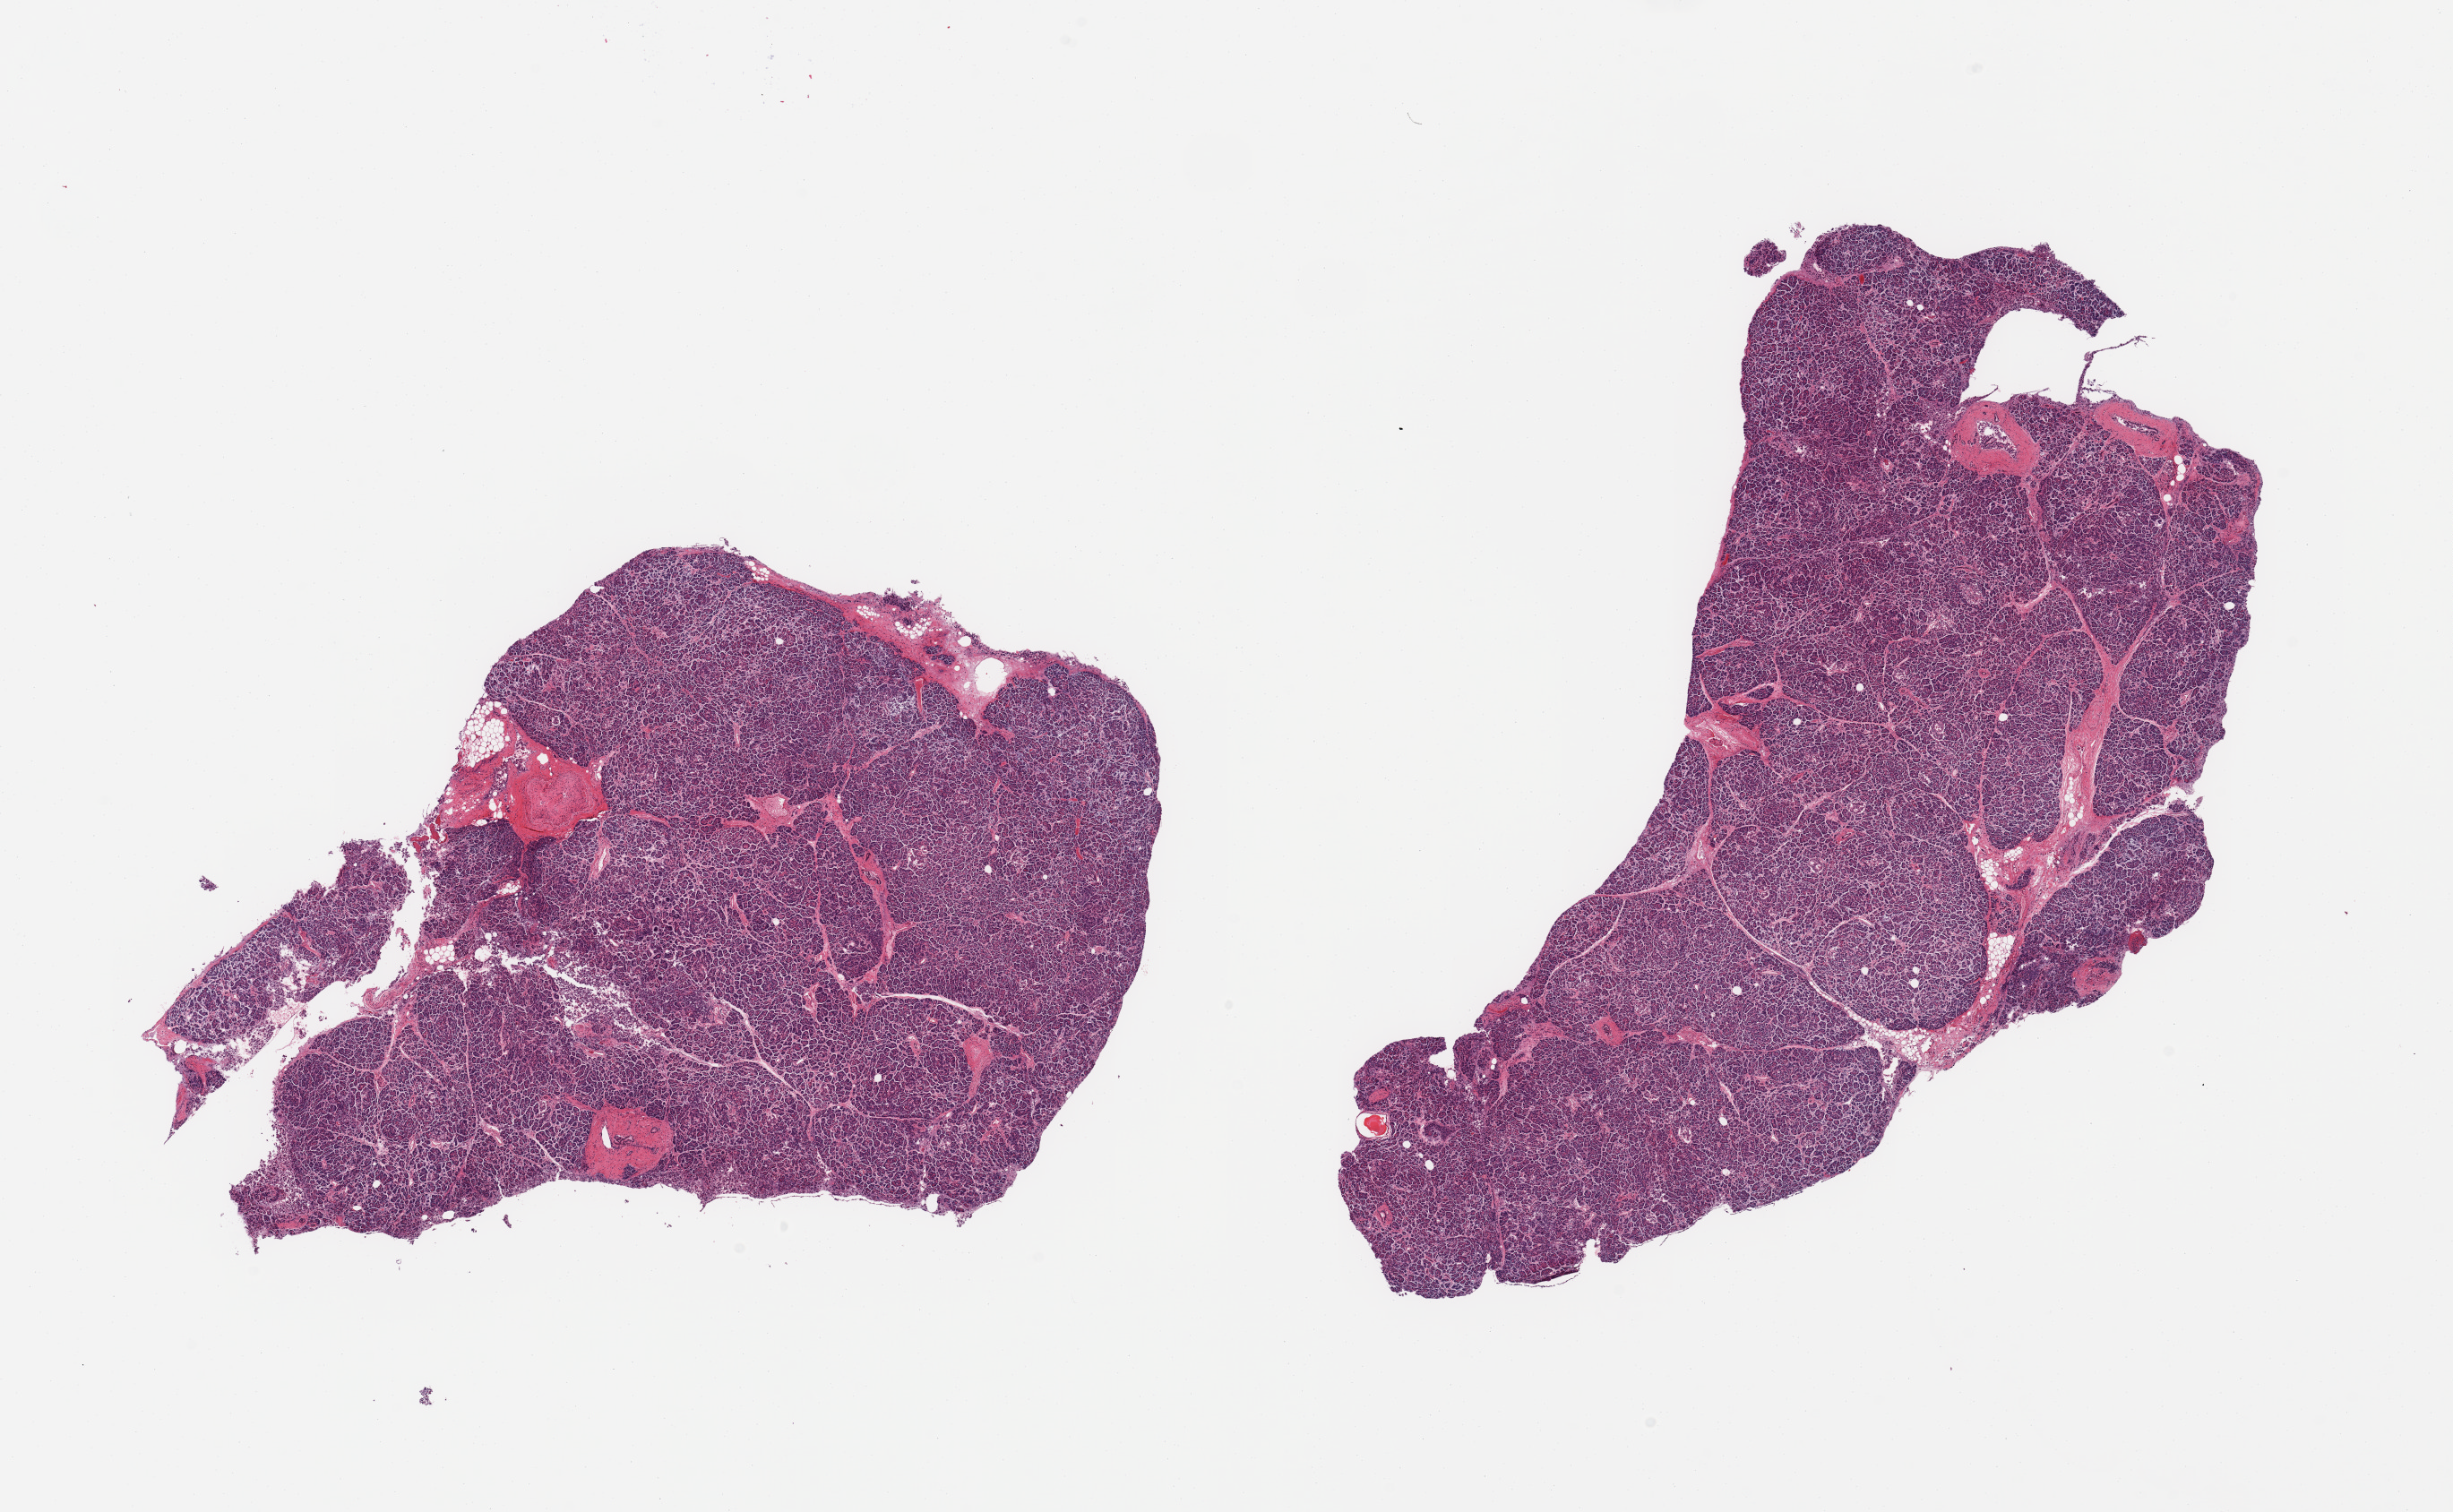
Digitized haematoxylin and eosin-stained section — whole scanned area (about 21.7 x 13.4 mm, acquisition: 20x scan) shown as a low-resolution overview, PAXgene-fixed, paraffin-embedded tissue, target tissue: pancreas, tissue donor sample.
Review note (as recorded): 2 pieces; moderate autolysis focally.